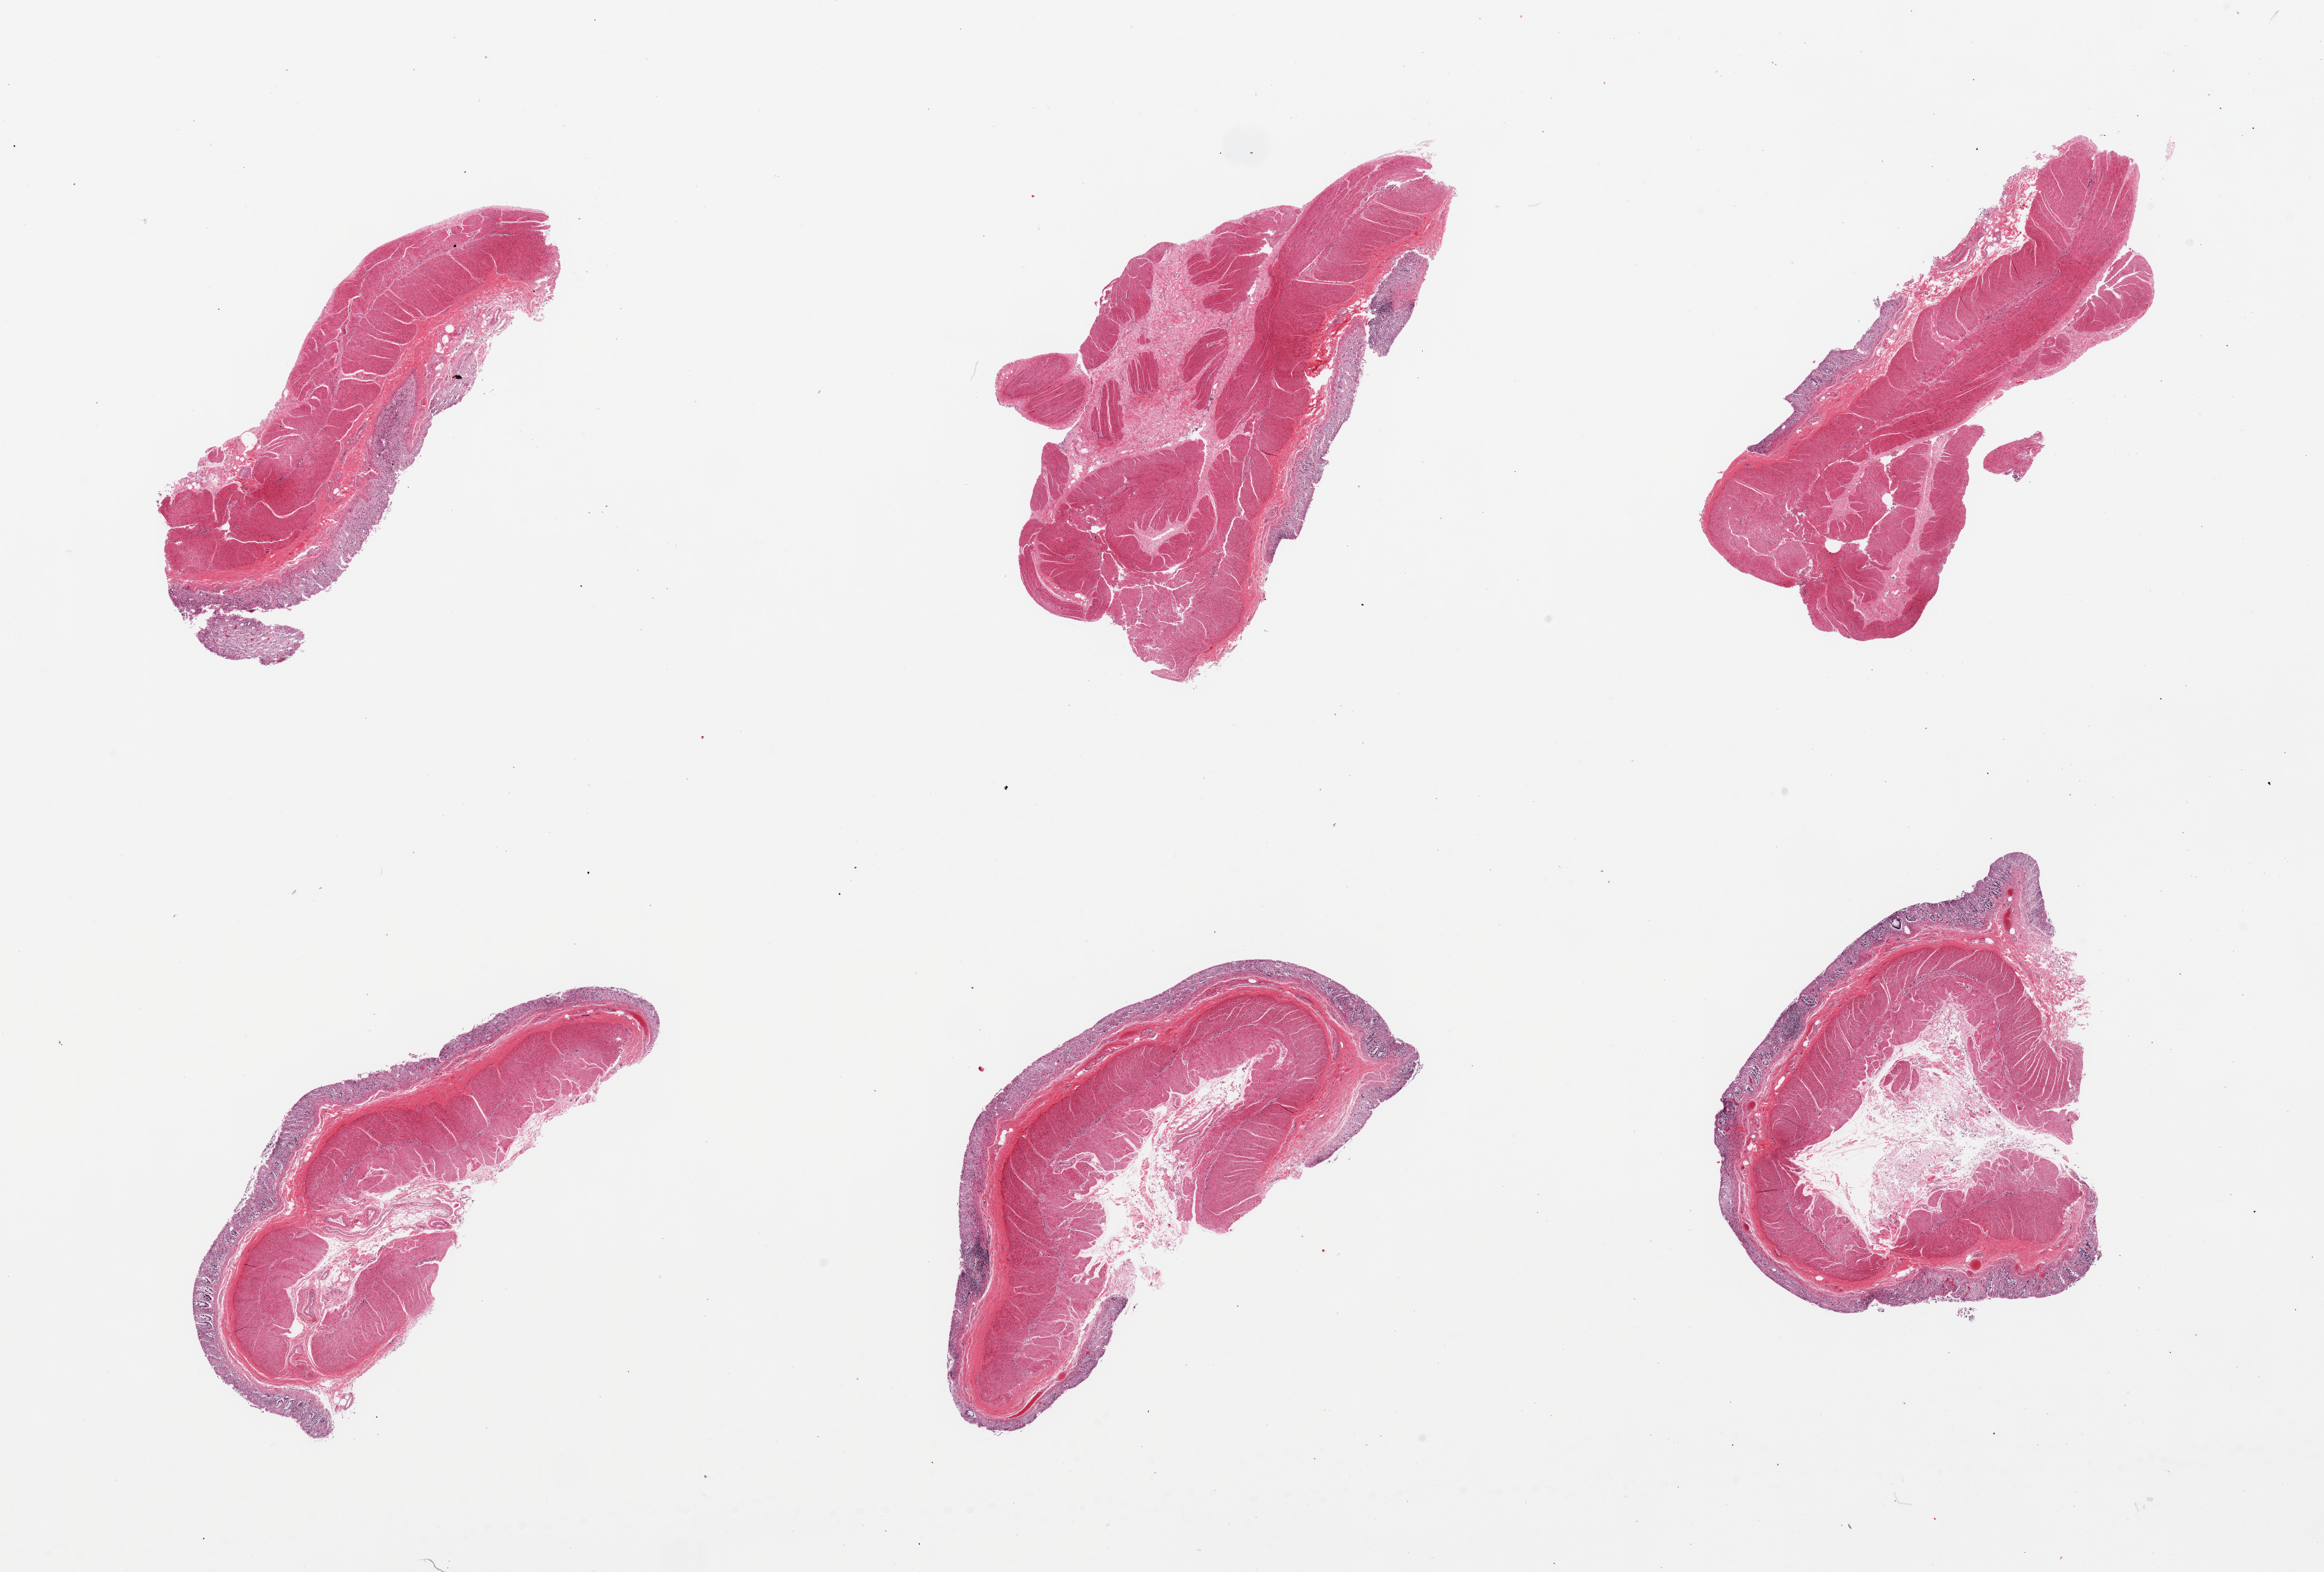
Digitized H&E-stained section, brightfield, whole scanned area (about 29.5 x 20.0 mm) shown as a low-resolution overview, PAXgene-fixed, paraffin-embedded tissue, target tissue: sigmoid colon, tissue donor sample. Donor sex: female.
Pathologist's review note for this sample: 6 pieces, all have adherent mucosa, completely autolyzed/sloughed.